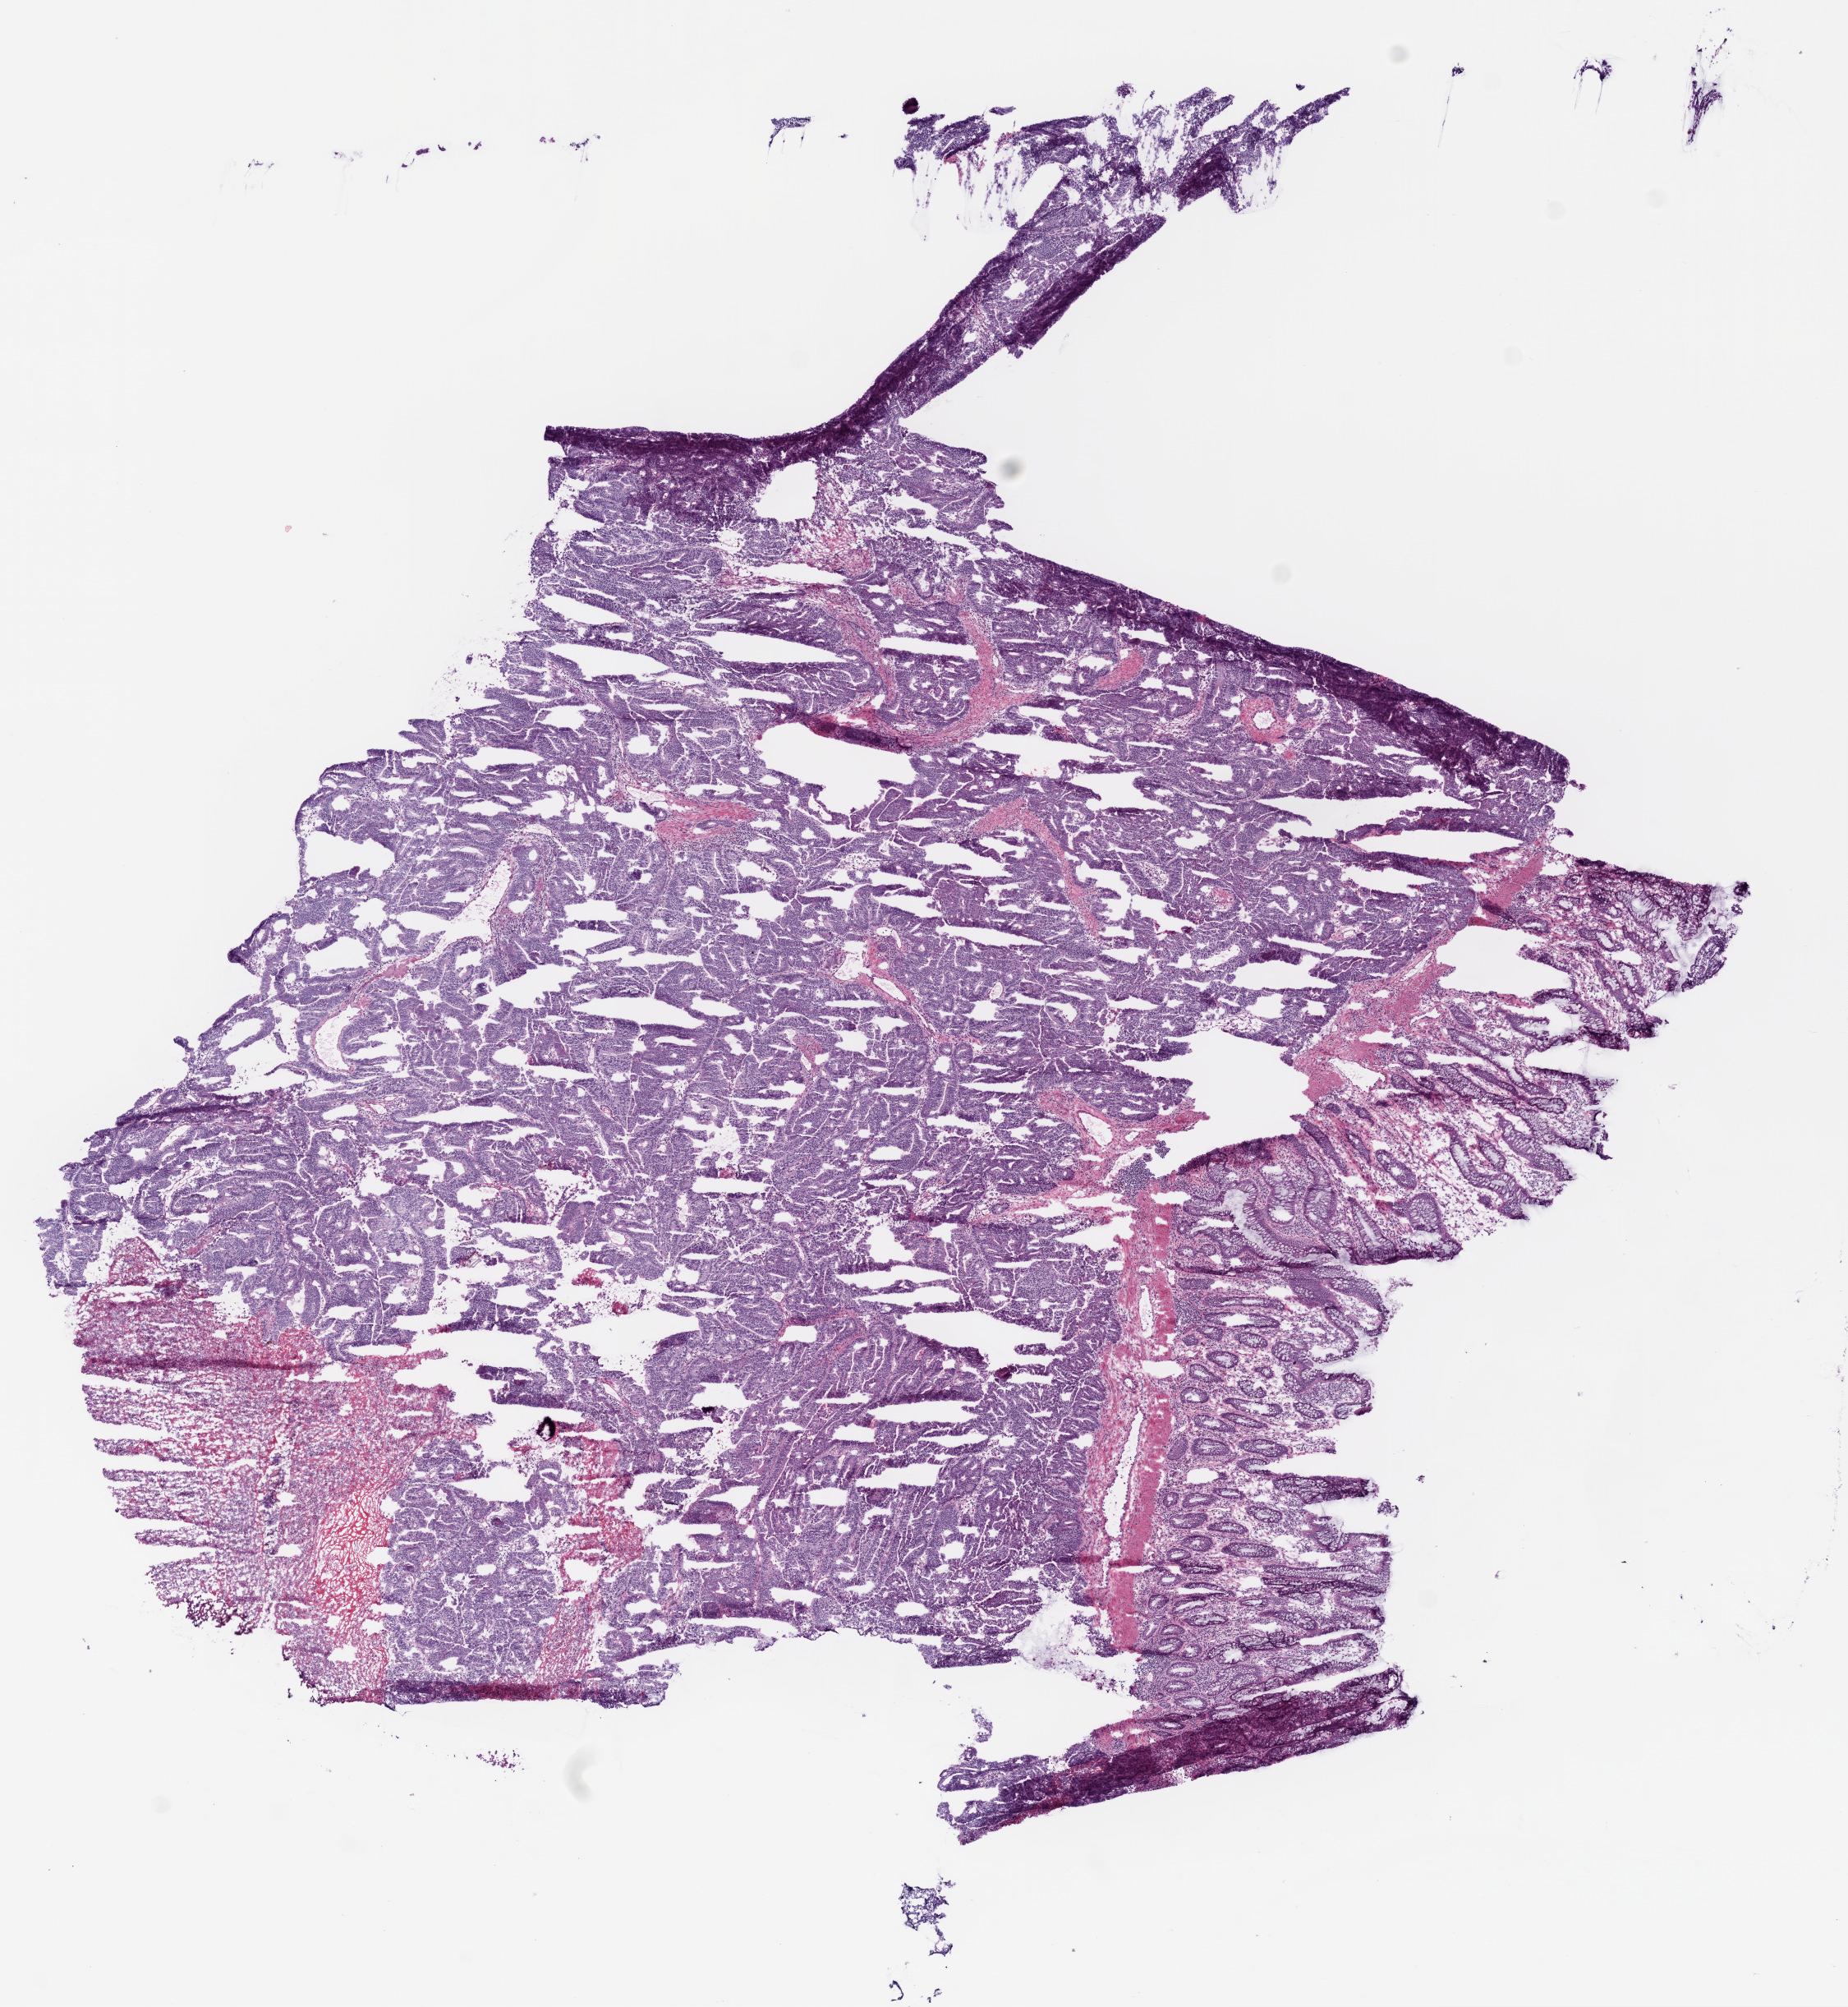
Digitized Hematoxylin and eosin (H&E) stained tissue section (whole slide), whole scanned area (about 9.0 x 9.8 mm) shown as a low-resolution overview. Frozen section from the bottom of the tissue portion. Primary tumour sample from the rectum. Female patient; age at initial diagnosis 85 years. Composition of this section per pathologist review: tumour cells 82%, tumour nuclei 93%.
Histologic diagnosis: Adenocarcinoma, NOS (rectosigmoid junction).